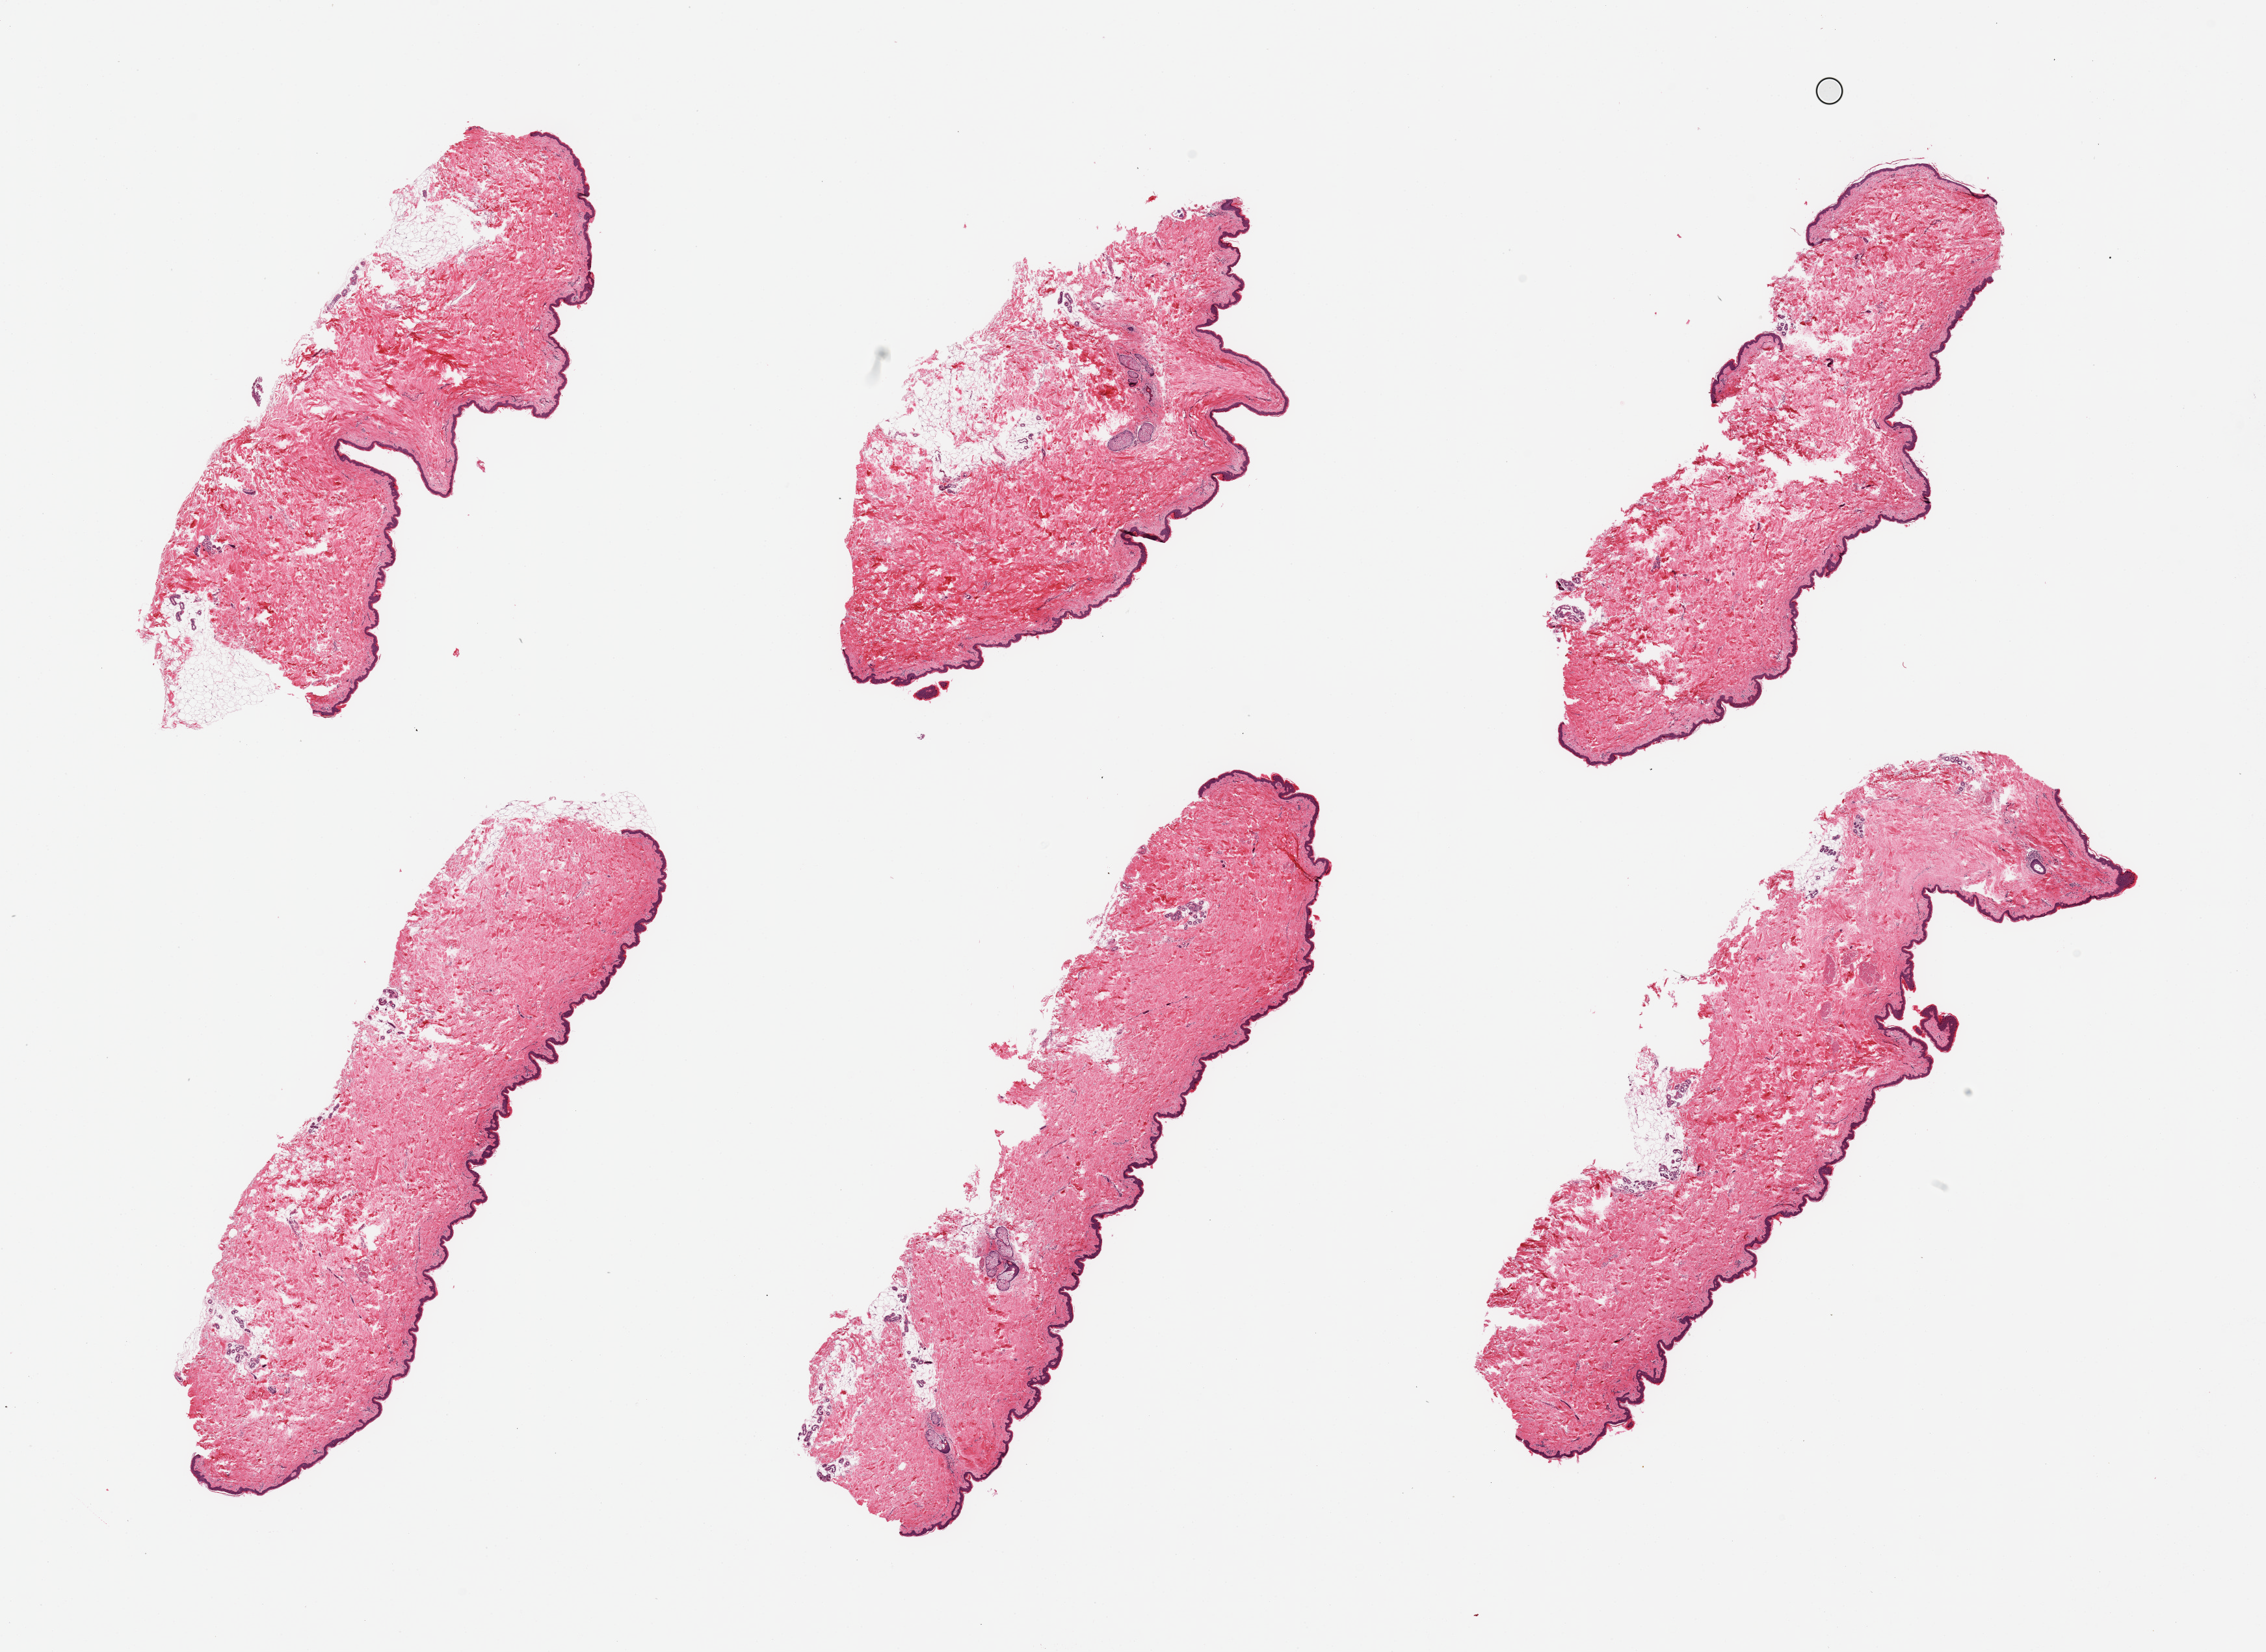
H&E whole-slide image, brightfield — shown as a low-resolution overview of the whole scanned area (about 27.6 x 20.1 mm). PAXgene-fixed paraffin-embedded (PFPE) section. Target tissue: skin of suprapubic region. Tissue donor sample. Female donor.
* reviewer comment on this tissue sample: 6 pieces; generally well trimmed; 10% dermal fat